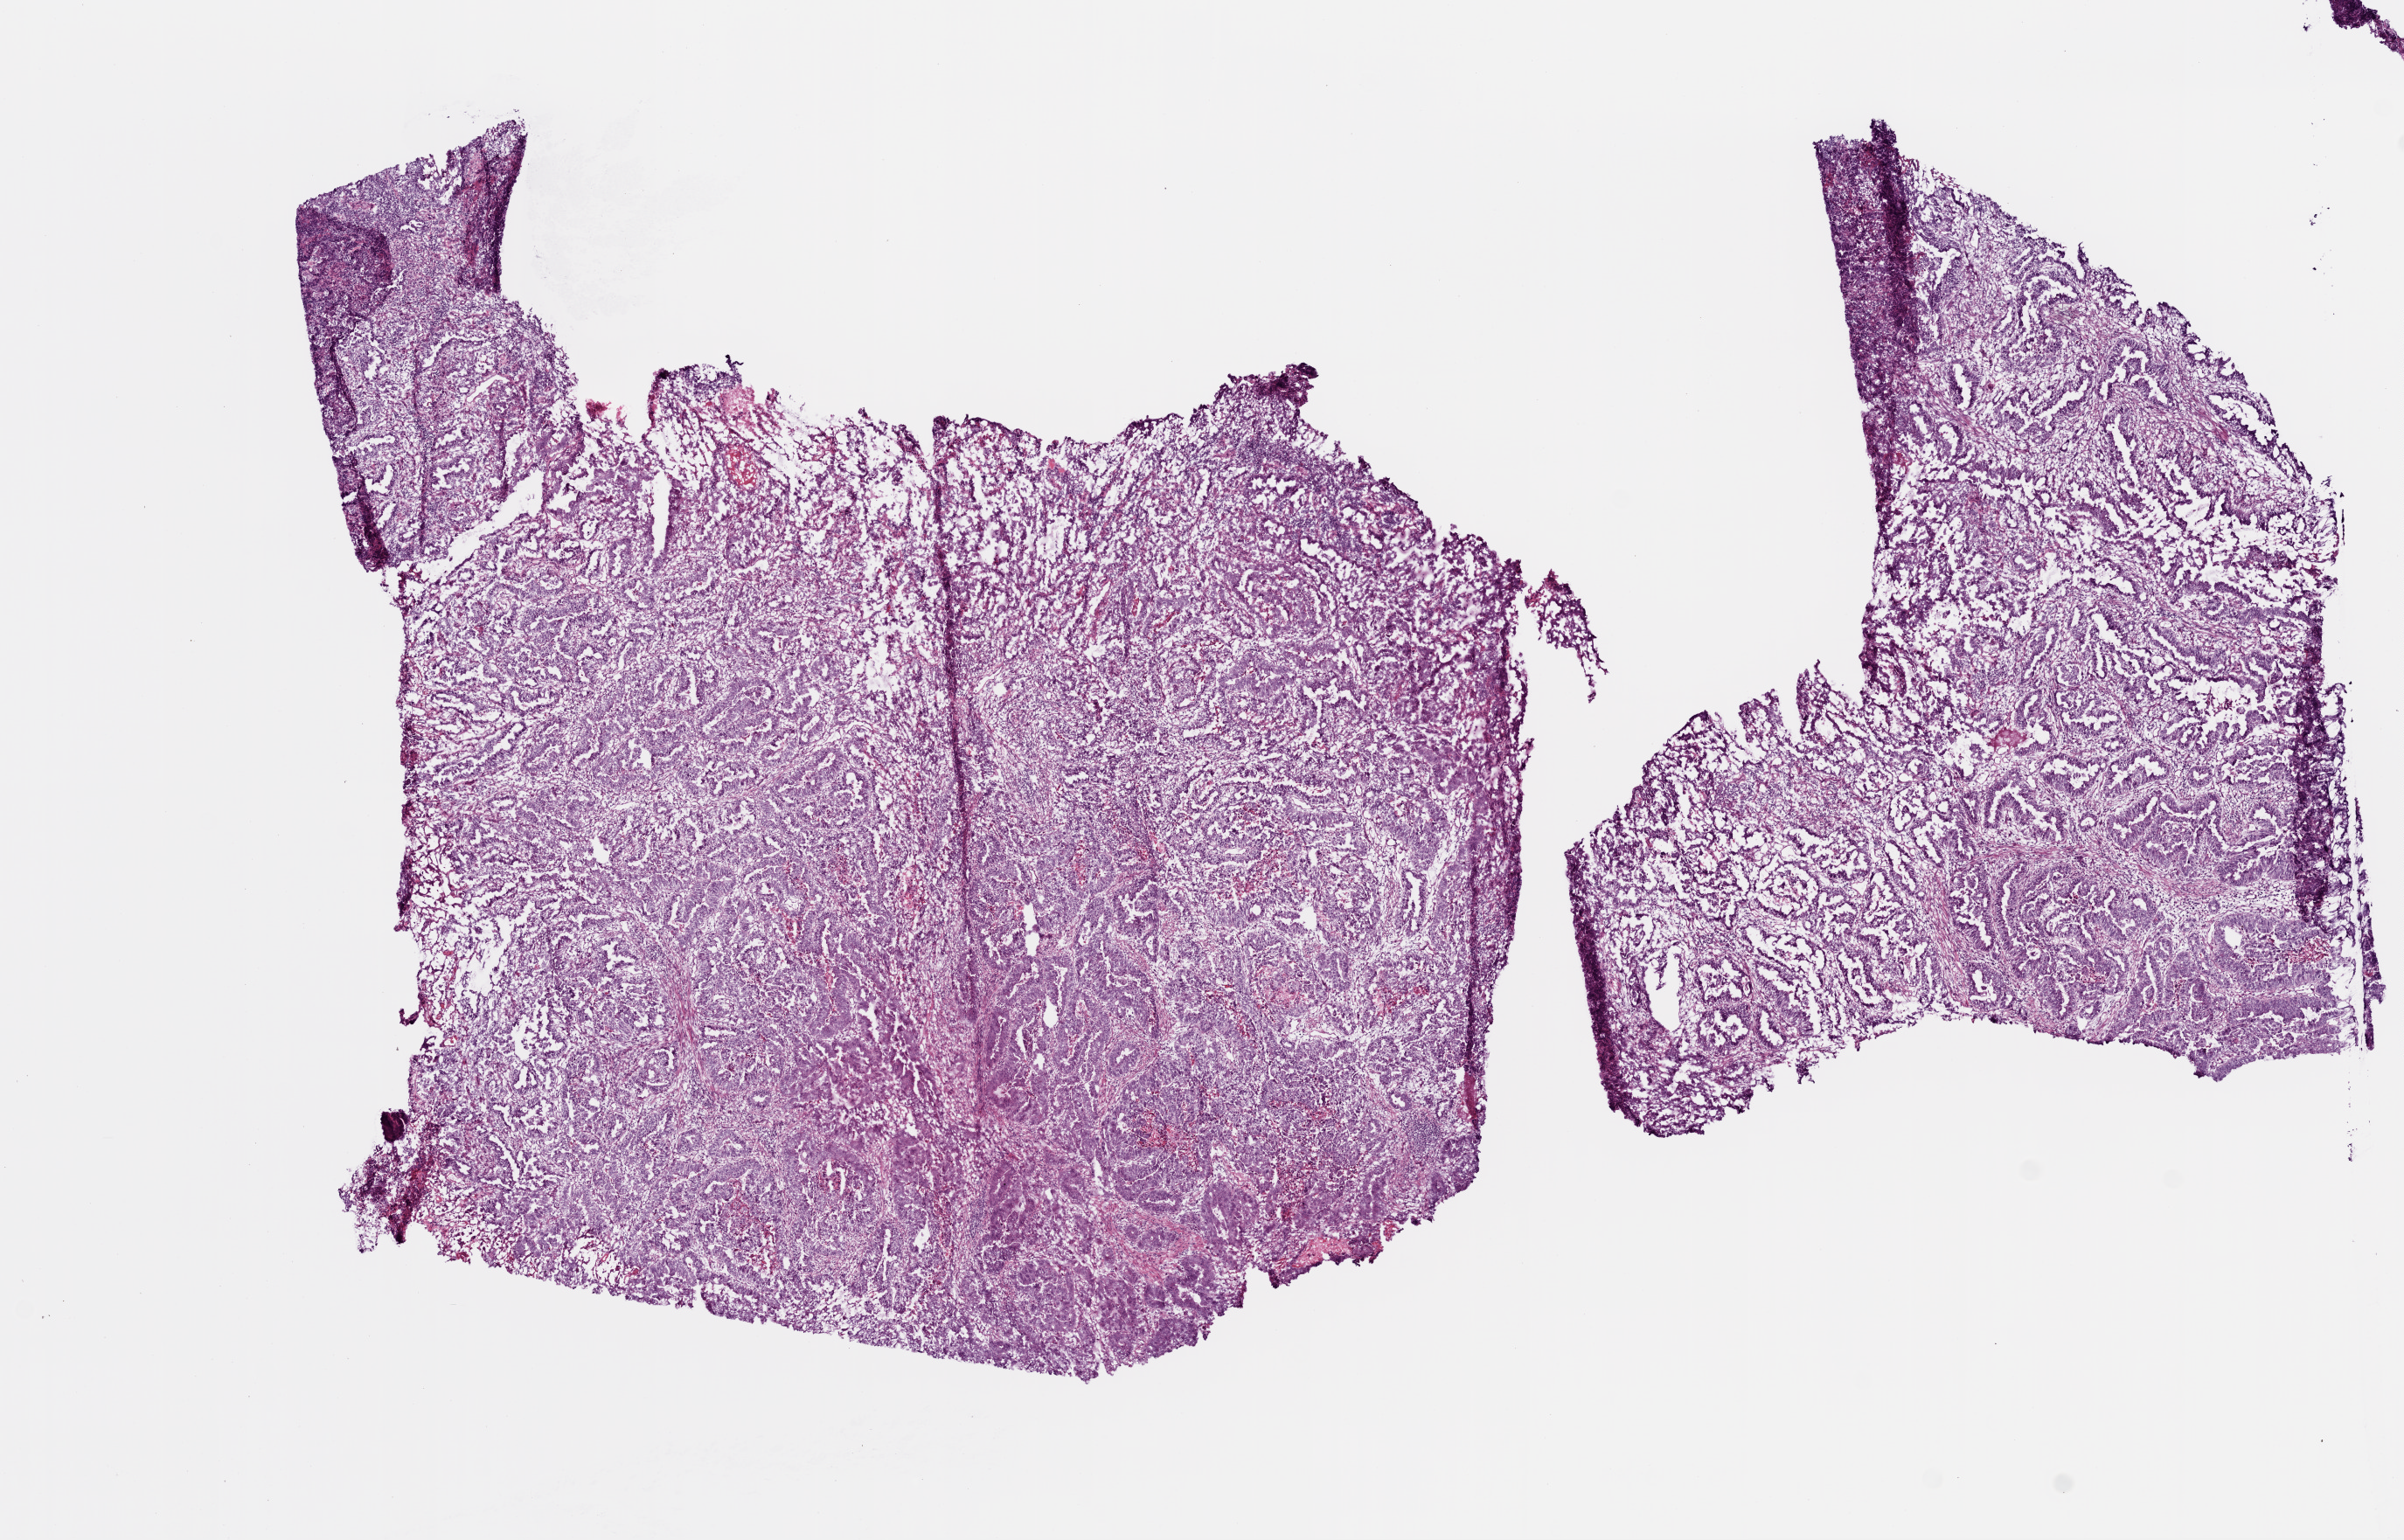
H&E-stained whole-slide image, a low-resolution overview of the entire scanned area, about 11.0 x 7.1 mm; frozen section from the top of the tissue portion; primary tumour sample from the stomach. Patient: female, age at initial diagnosis 80 years. Histologic grade: G2 (moderately differentiated). Composition of this section per pathologist review: tumour cells 70%, tumour nuclei 80%, normal cells 0%, stromal cells 15%, necrosis 15%.
Diagnosis: Adenocarcinoma, intestinal type (cardia, NOS). Lymph nodes positive (case pathology): 6 of 15 examined. AJCC pathologic stage: IV (5th edition).